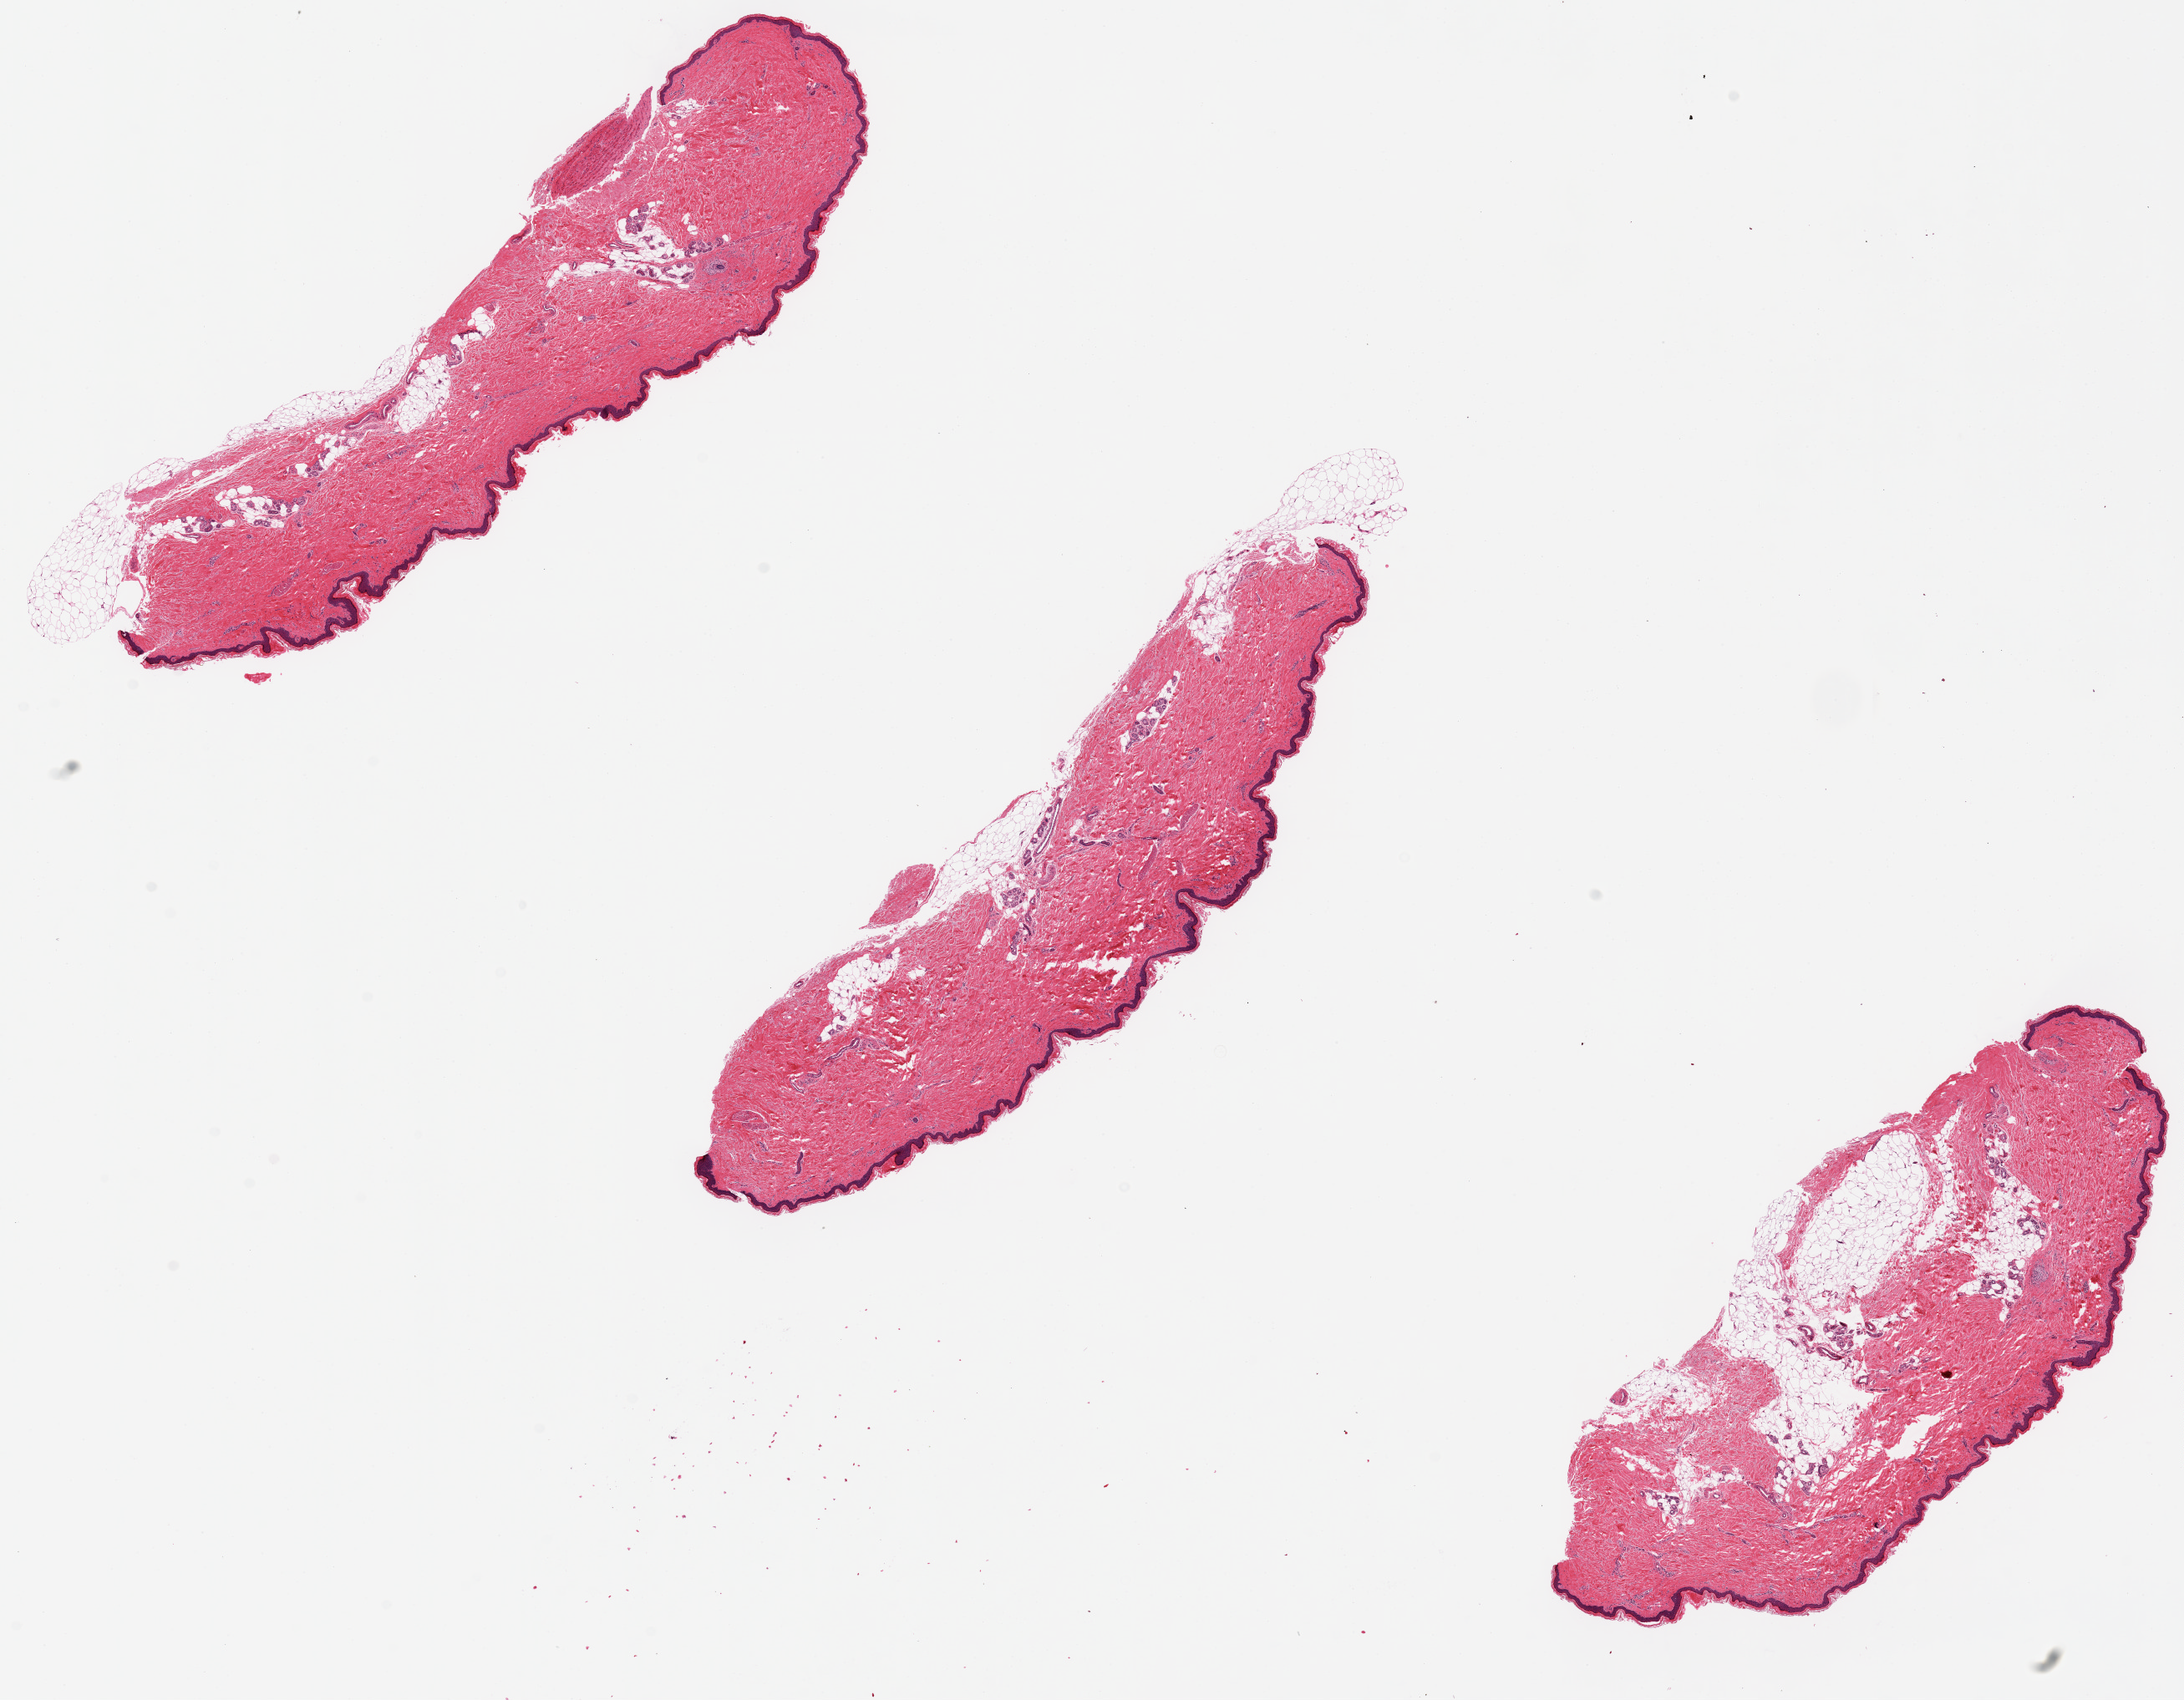
H&E whole-slide image, brightfield — whole scanned area (about 20.7 x 16.1 mm, acquisition: 20x scan) shown as a low-resolution overview. PAXgene-fixed paraffin-embedded (PFPE) section. Sampled site (target tissue): skin of lower leg. Tissue donor sample. Donor: male.
Reviewer comment on this tissue sample: Epidermis is ~3-4% of total specimen thickness.